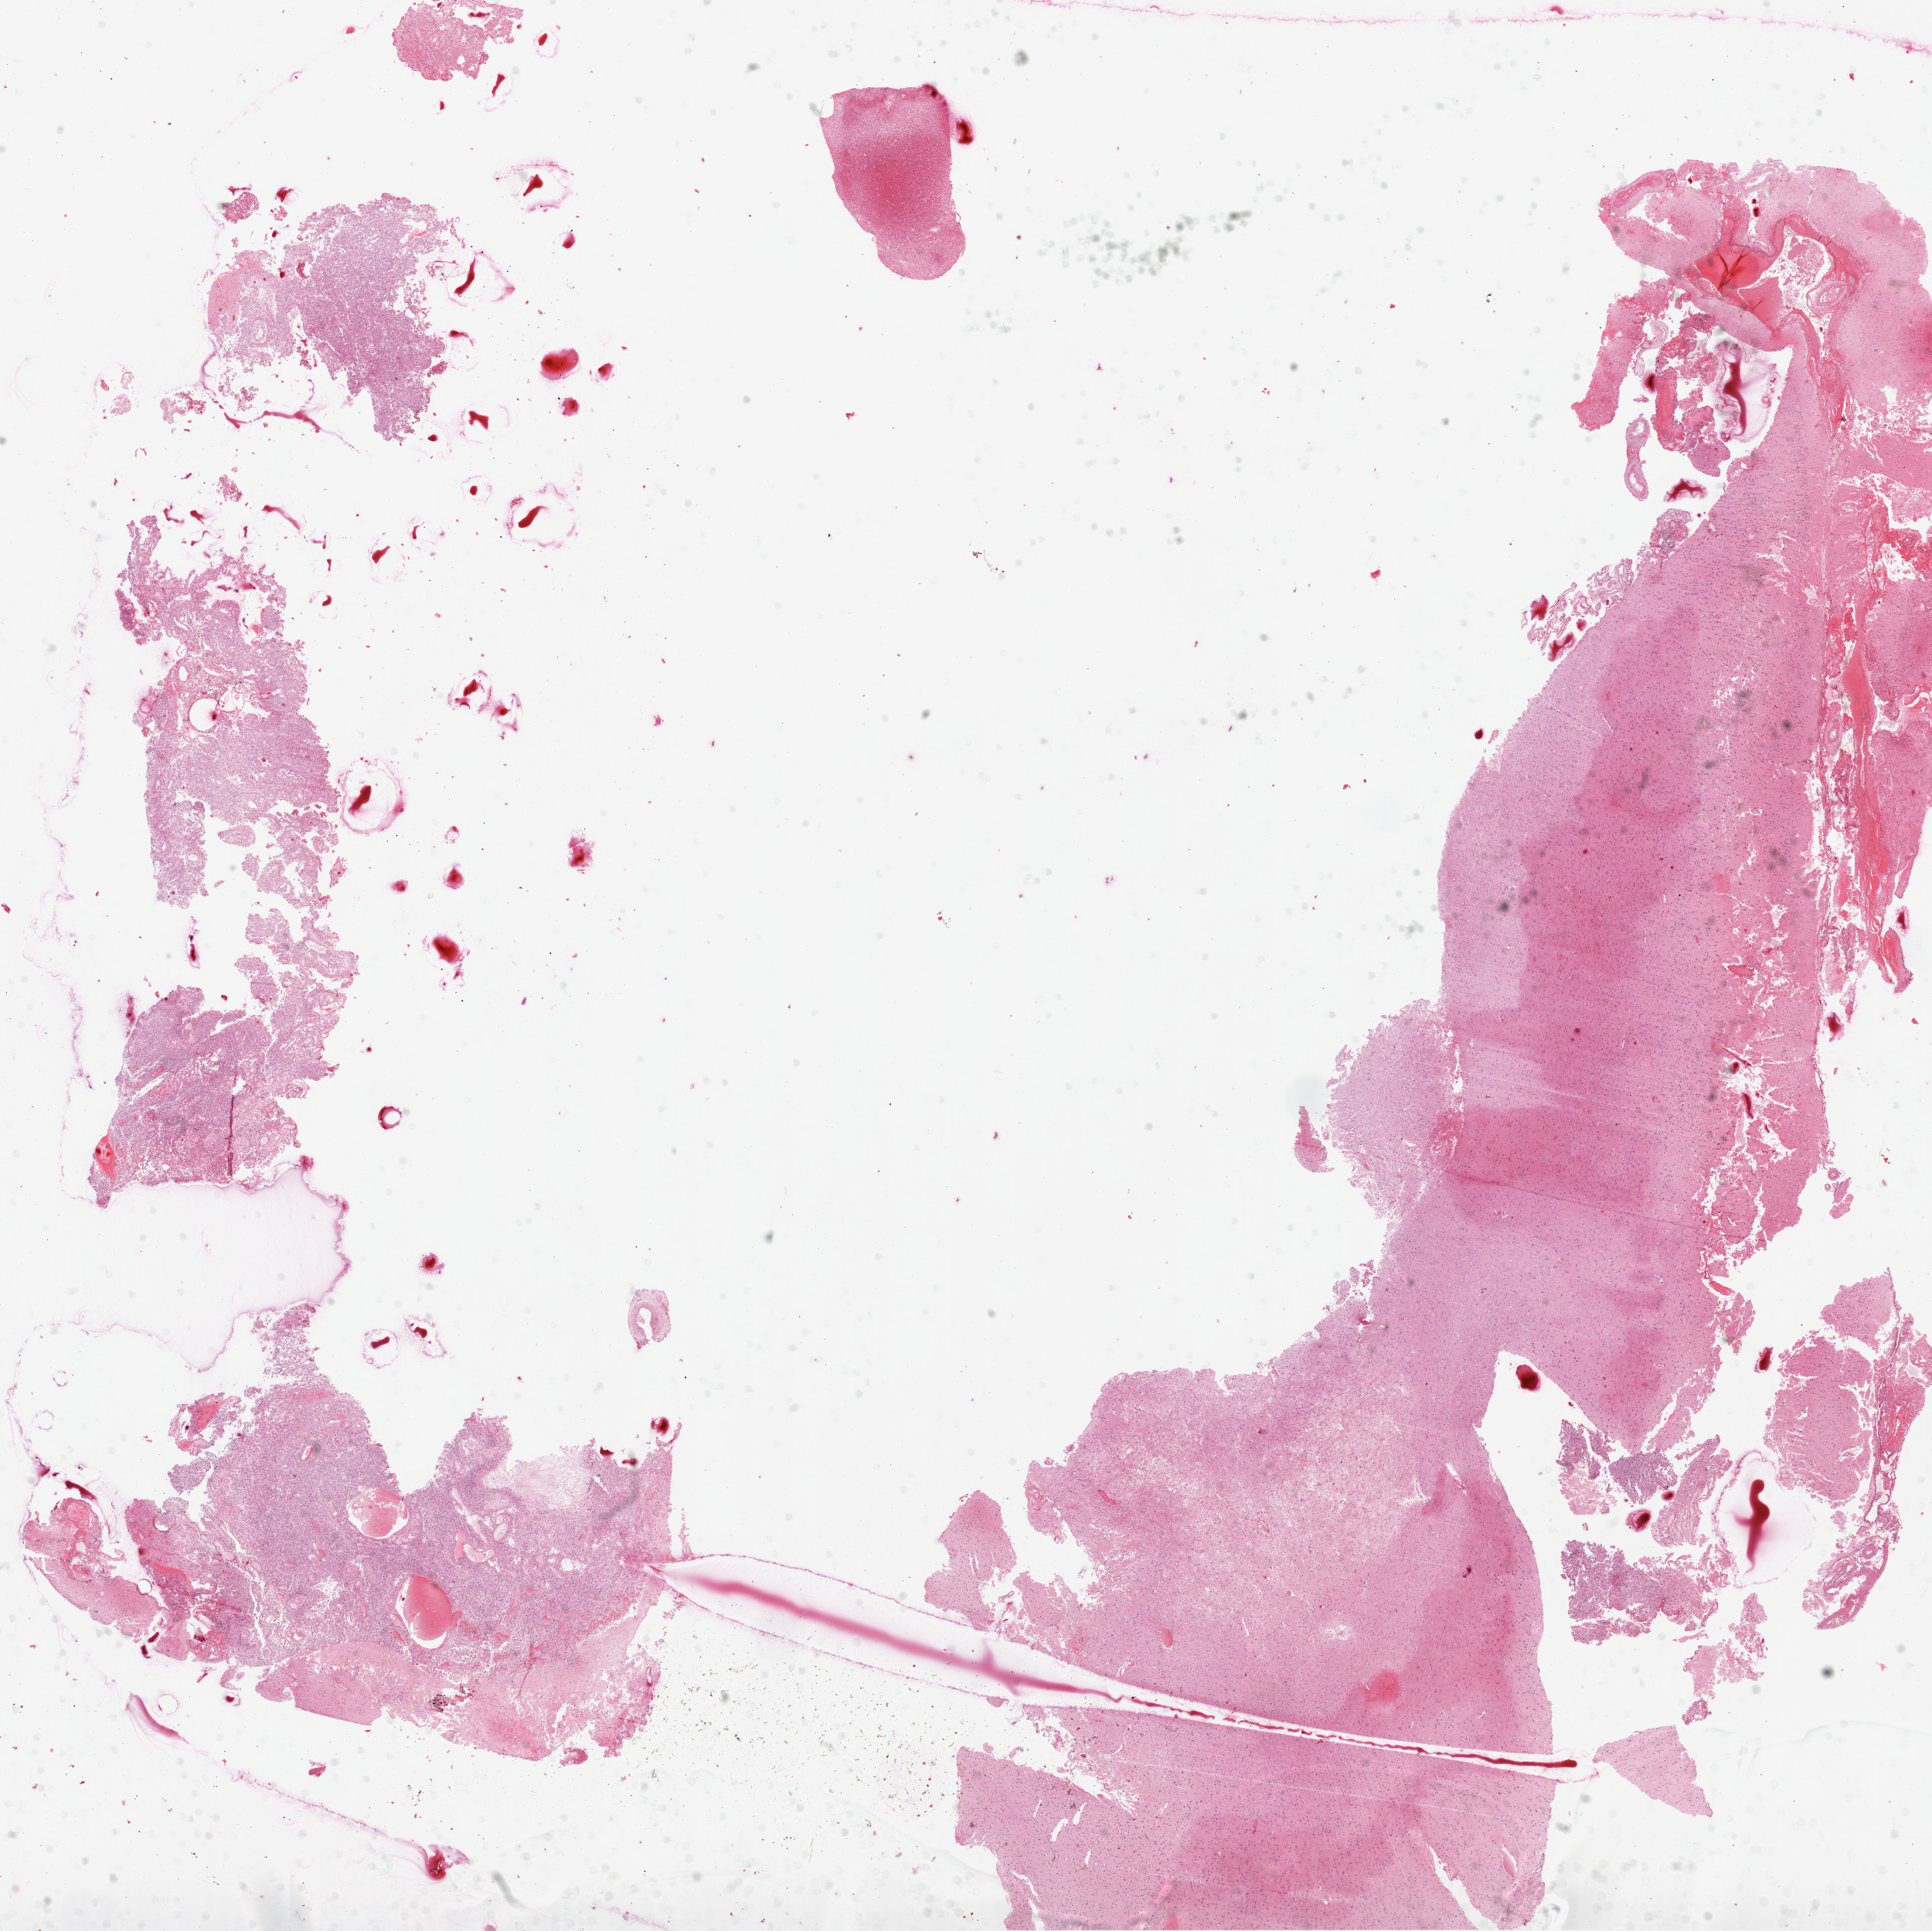
Digitized H&E-stained tissue section (whole slide), low-resolution overview of the scanned area, about 20.1 x 20.1 mm (from a 20x scan). Formalin-fixed paraffin-embedded (FFPE) diagnostic section. Primary tumour sample from the brain. Male, age 66 years at initial diagnosis.
Diagnosis: Glioblastoma.